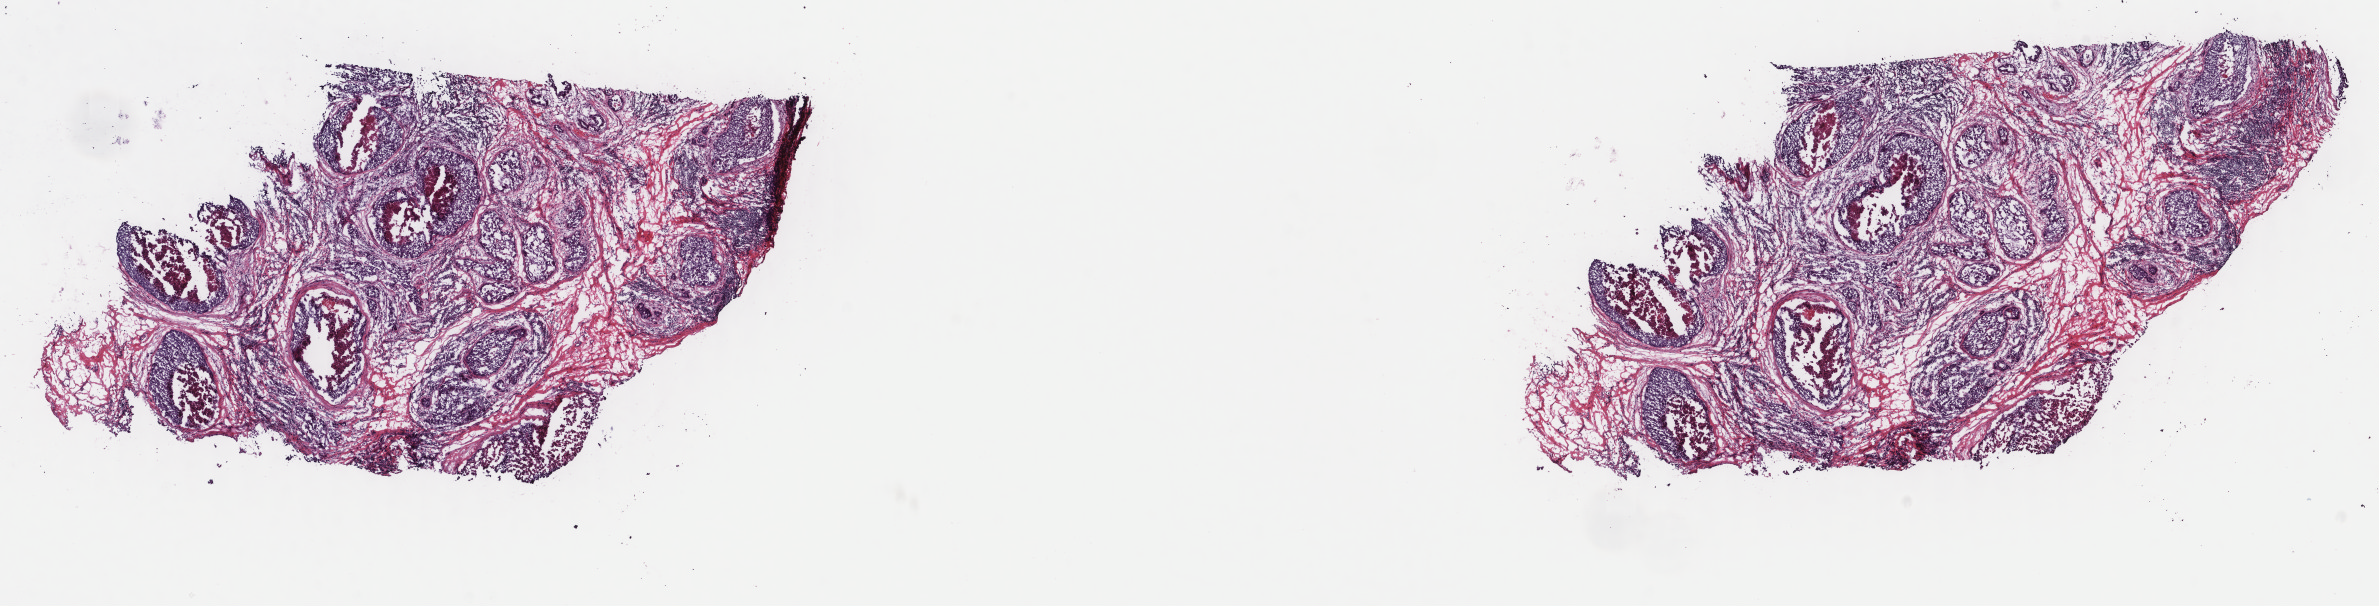
Whole-slide histology image, H&E-stained, whole scanned area (about 18.9 x 4.8 mm) shown as a low-resolution overview, frozen section, primary tumour sample from the uterus. Patient: female, age at initial diagnosis 65 years. Histologic grade: G3 (poorly differentiated). Composition of this section per pathologist review: tumour cells 60%, tumour nuclei 60%, normal cells 0%, stromal cells 20%, necrosis 20%. Infiltration values recorded for this section: lymphocyte infiltration 40%, monocyte infiltration 20%, neutrophil infiltration 20%.
Histologic diagnosis: Endometrioid adenocarcinoma, NOS (endometrium). FIGO stage: IIIA.